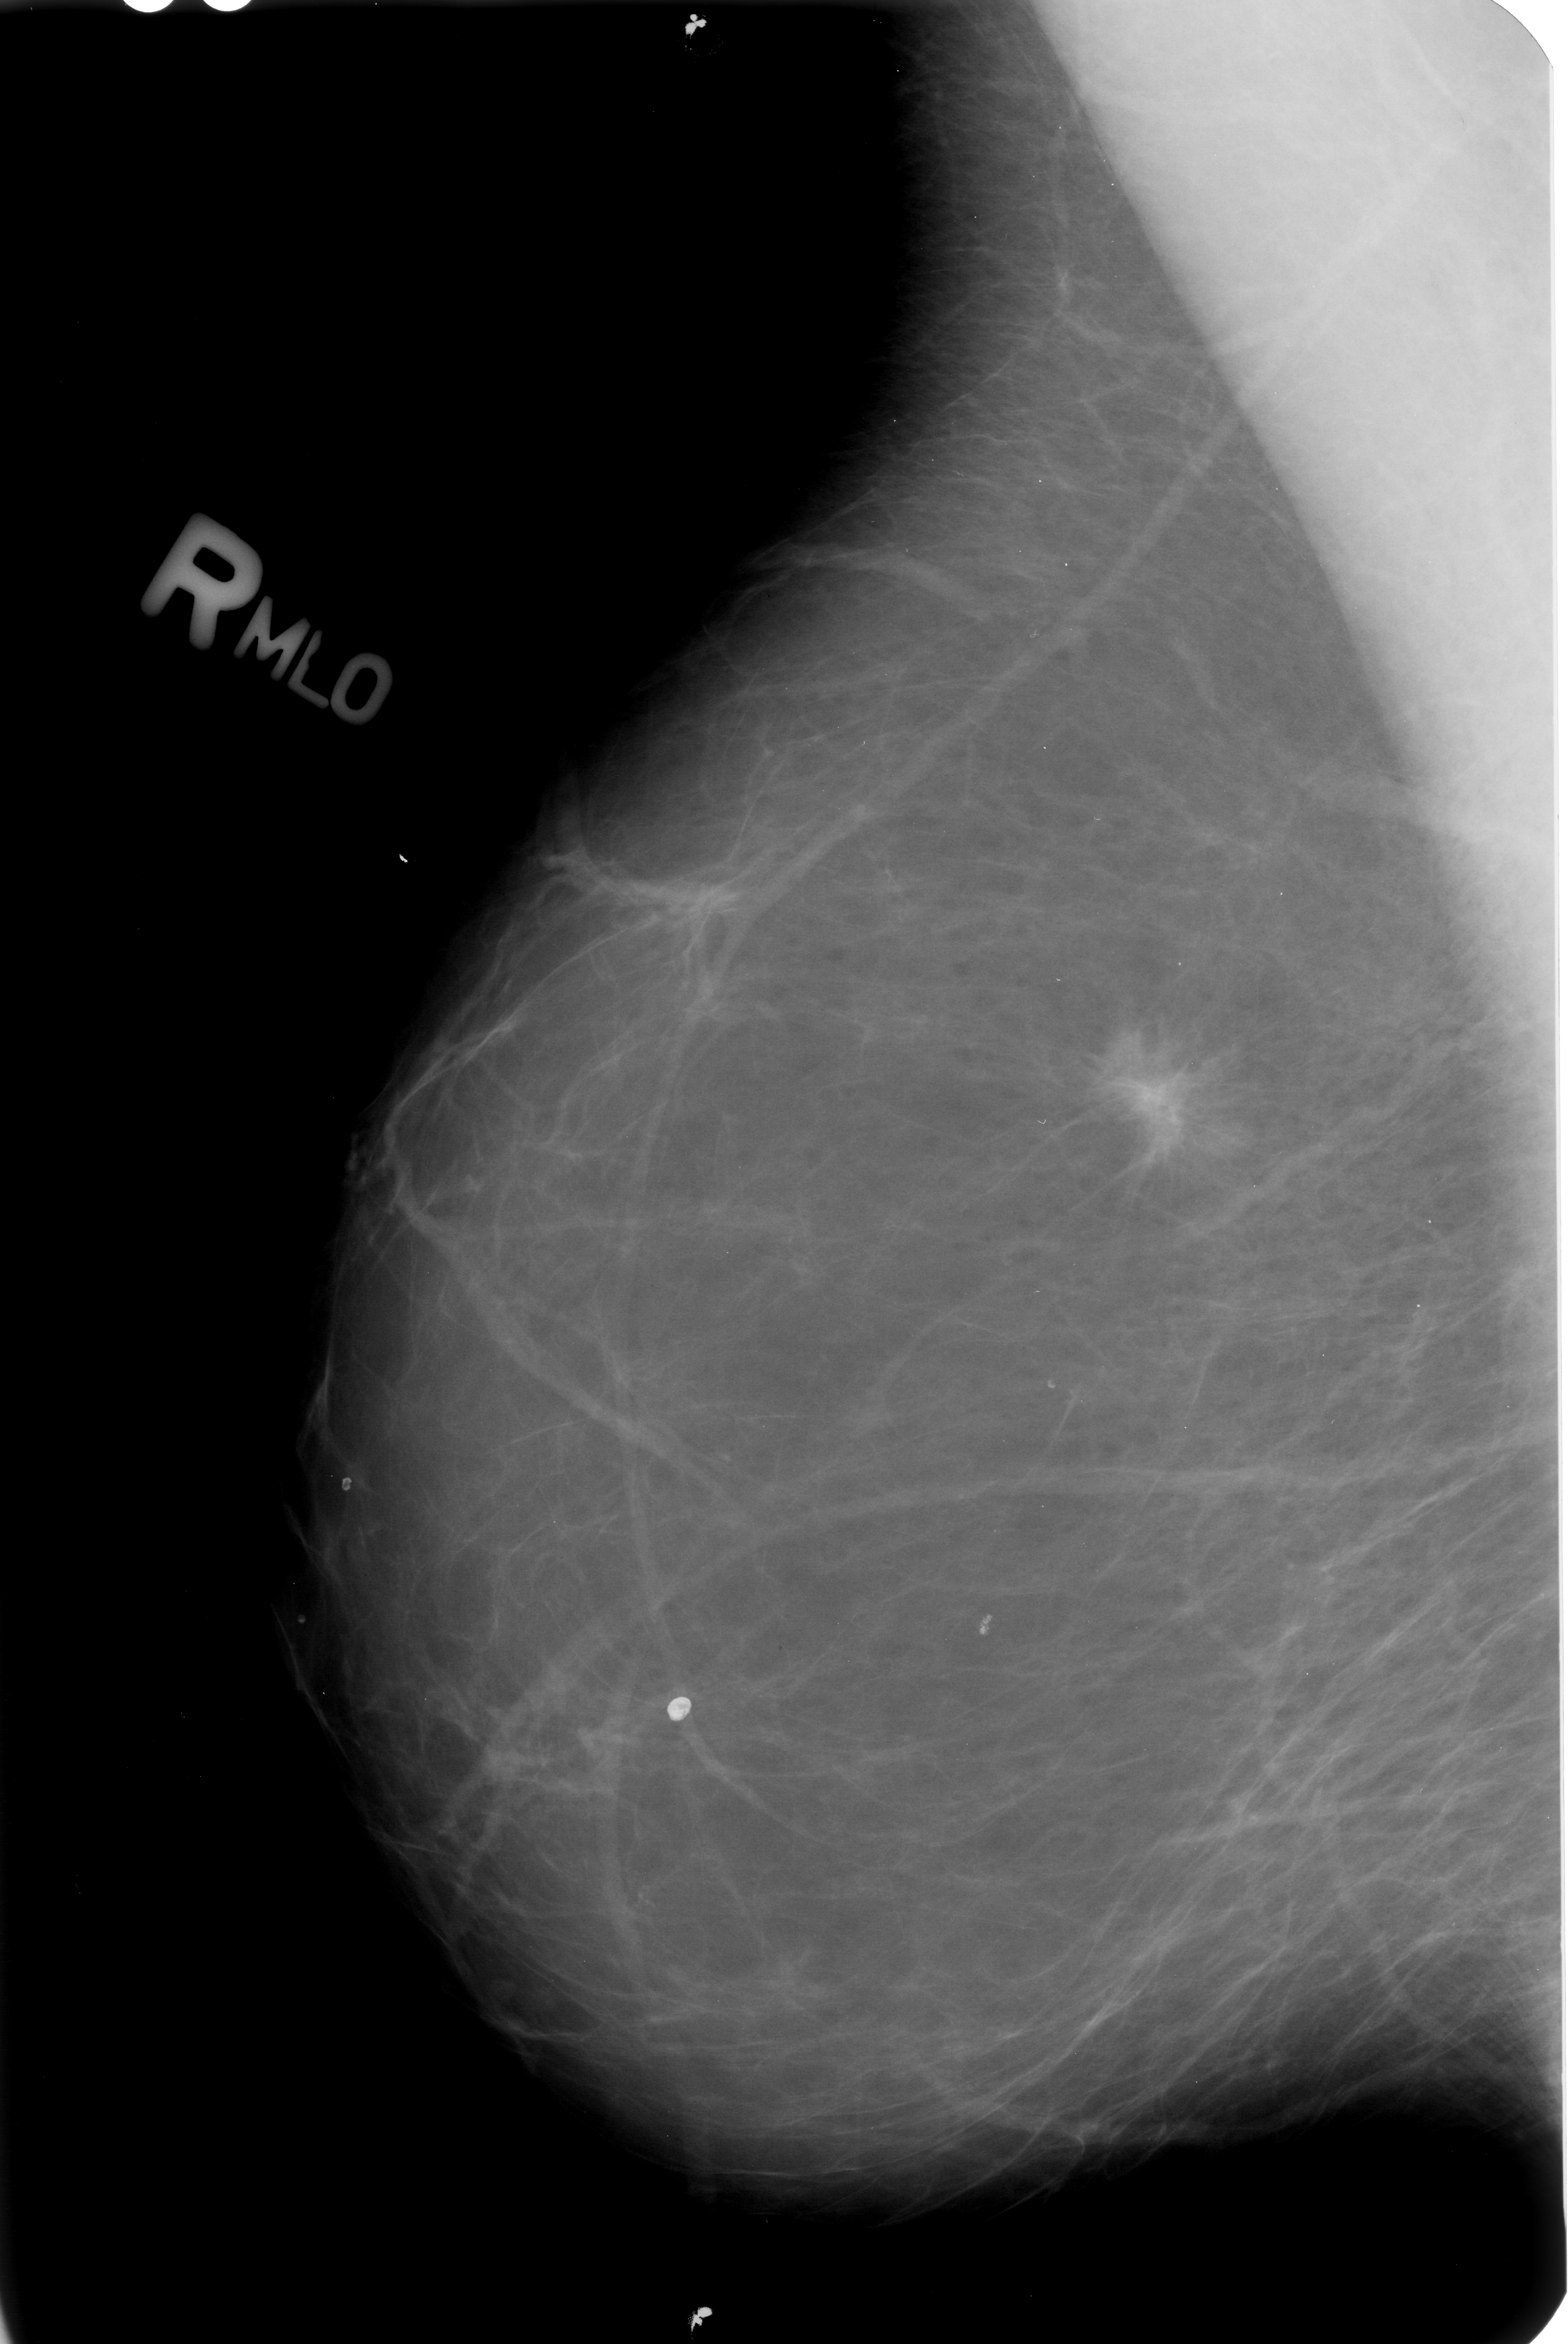
Mammogram (digitized film); right breast; mediolateral oblique (MLO) view; breast composition: almost entirely fatty (BI-RADS density category 1 of 4).
Marked findings (only marked abnormalities are described; nothing is implied about the rest of the image): mass, shape irregular / architectural distortion, margins spiculated; BI-RADS assessment category 5; subtlety rating 5 on a 1 (subtle) to 5 (obvious) scale; pathology result (as recorded, not read from the image): malignant.